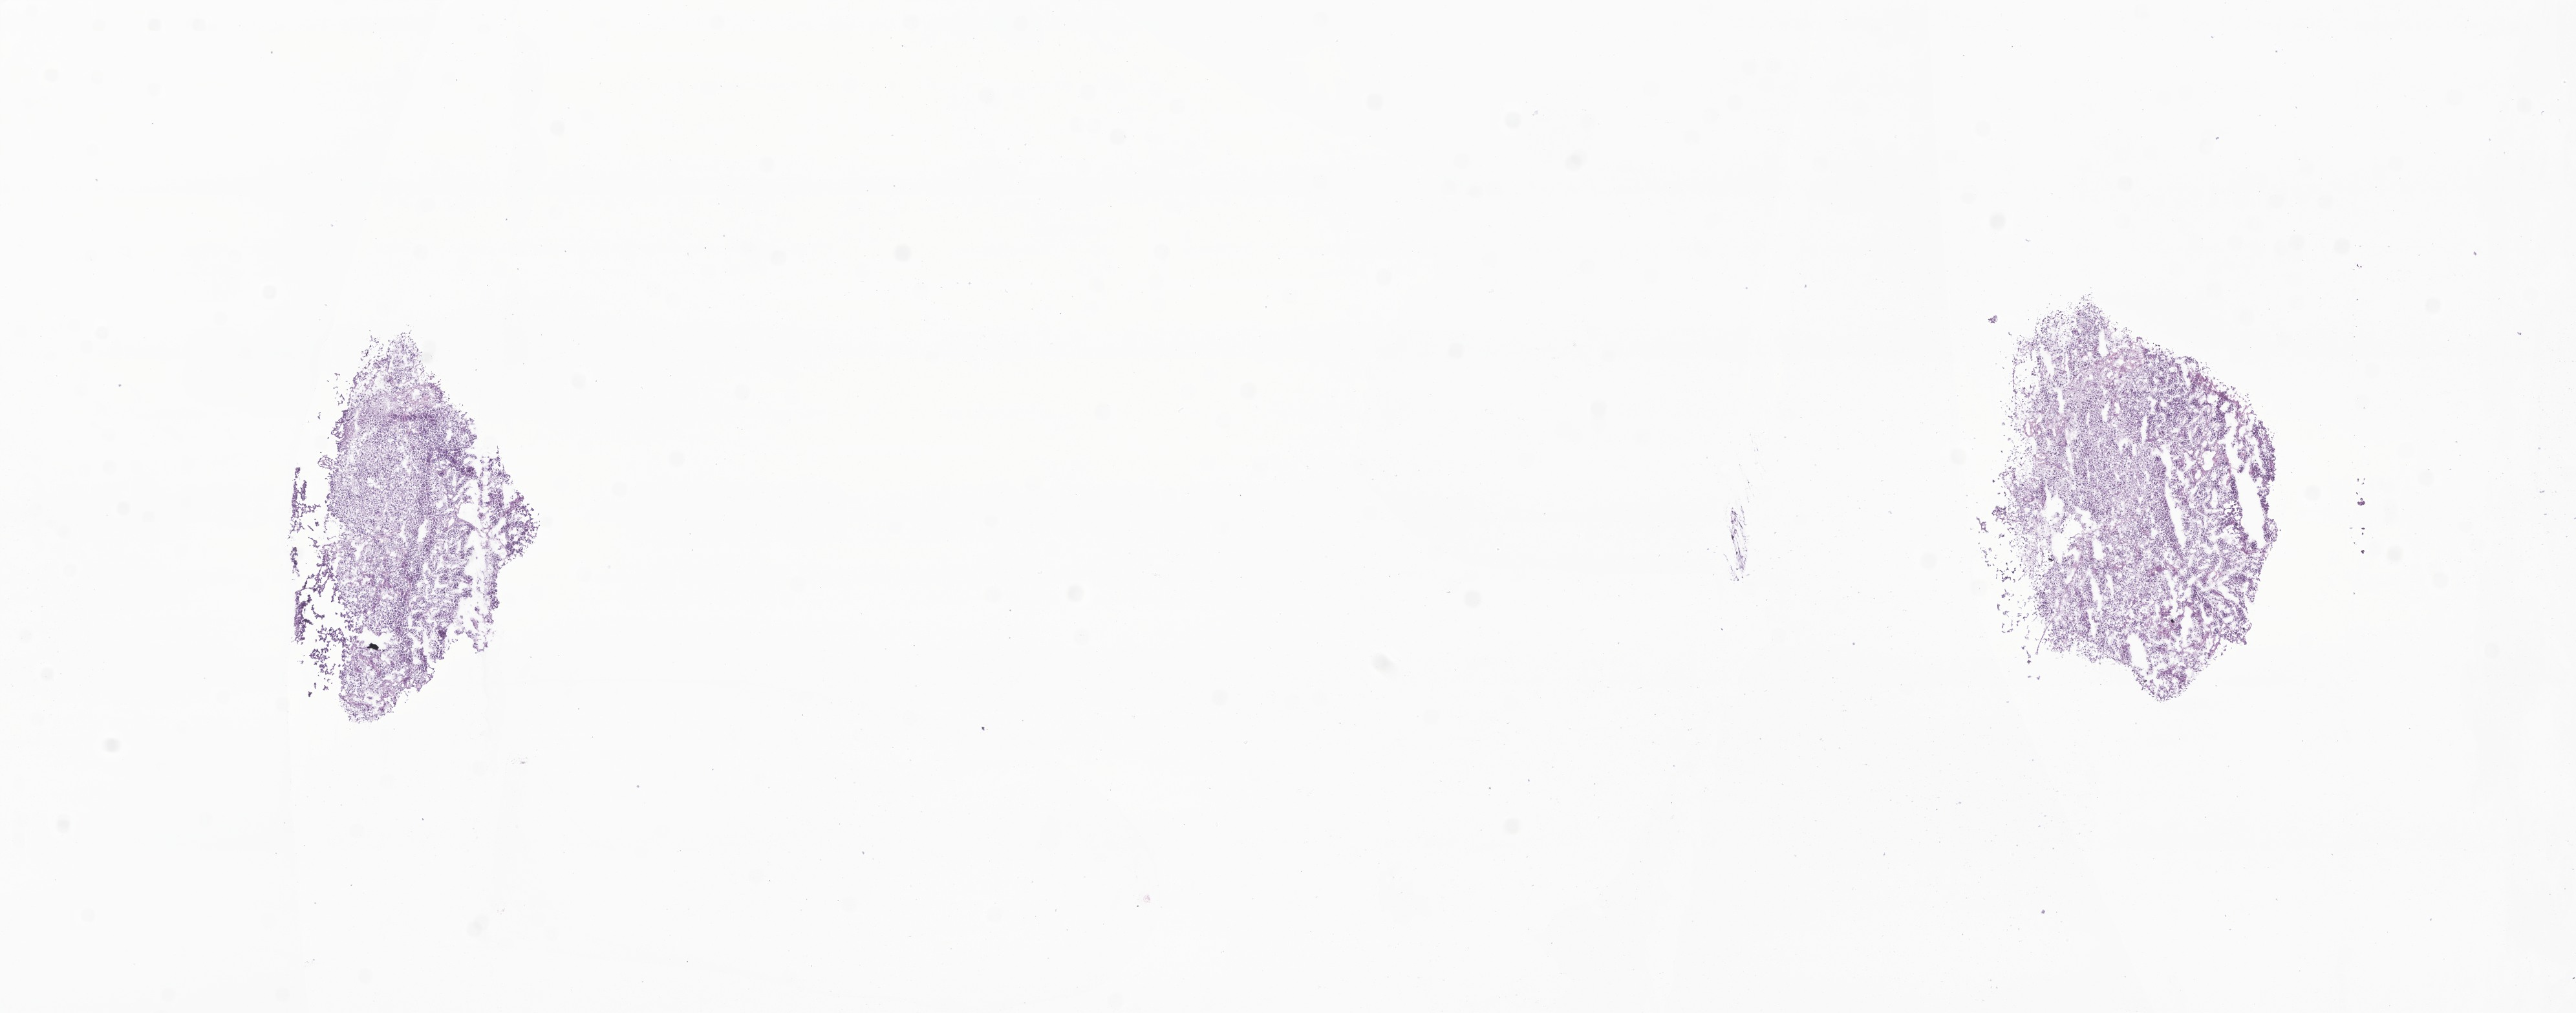
Whole-slide image, hematoxylin and eosin (H&E) stain of tumor tissue from the abdomen, low-resolution overview of the scanned area, about 16.8 x 6.6 mm, frozen section (OCT-embedded). Female patient, age 857 days (about 2.3 years).
Recorded diagnosis: Neuroblastoma, NOS.